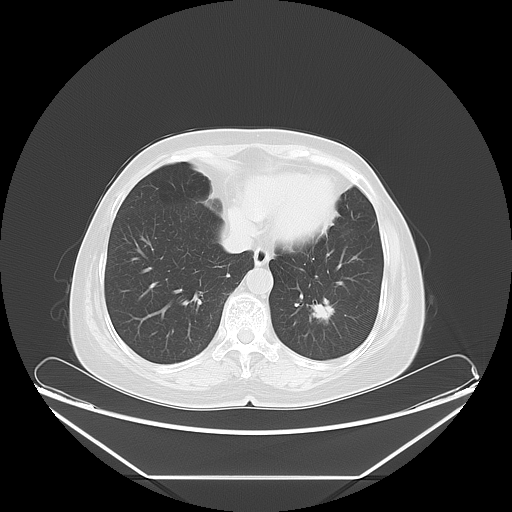
Chest CT, one axial slice. Position 19 of 61 along the scan axis. Reconstruction kernel LUNG. 120 kVp. Lung window (W 1500 / L -600 HU). 5 mm slice thickness. 512 × 512 image matrix, field of view 451 × 451 mm. Female patient, age 63 years. Case-level facts recorded for this patient, not image findings: clinical TNM (as recorded): T1c N0 M0.
Annotated regions visible in this slice (rectangle marked by the reading radiologist):
- lung tumour (recorded histology: adenocarcinoma): box from (x=308, y=295) to (x=336, y=330) px